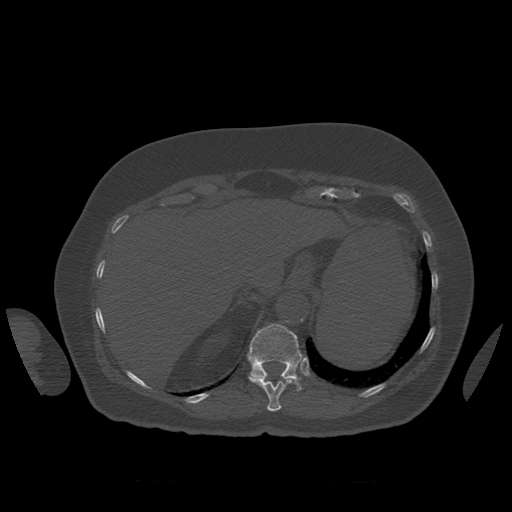
CT including the spine, one axial slice. Position 310 of 399 along the scan axis. Bone window (W 1800 / L 400 HU). 1.25 mm slice thickness. 512 × 512 image matrix, field of view 404 × 404 mm. Patient age 81 years. From the clinical record (not read from this slice): primary cancer: renal.
Annotated regions visible in this slice (semi-automatic segmentation, software-assisted and operator-edited):
- T11 vertebra: bounding box <249,377,293,412> (left, top, right, bottom; pixels)
- T12 vertebra: <247,324,303,391>